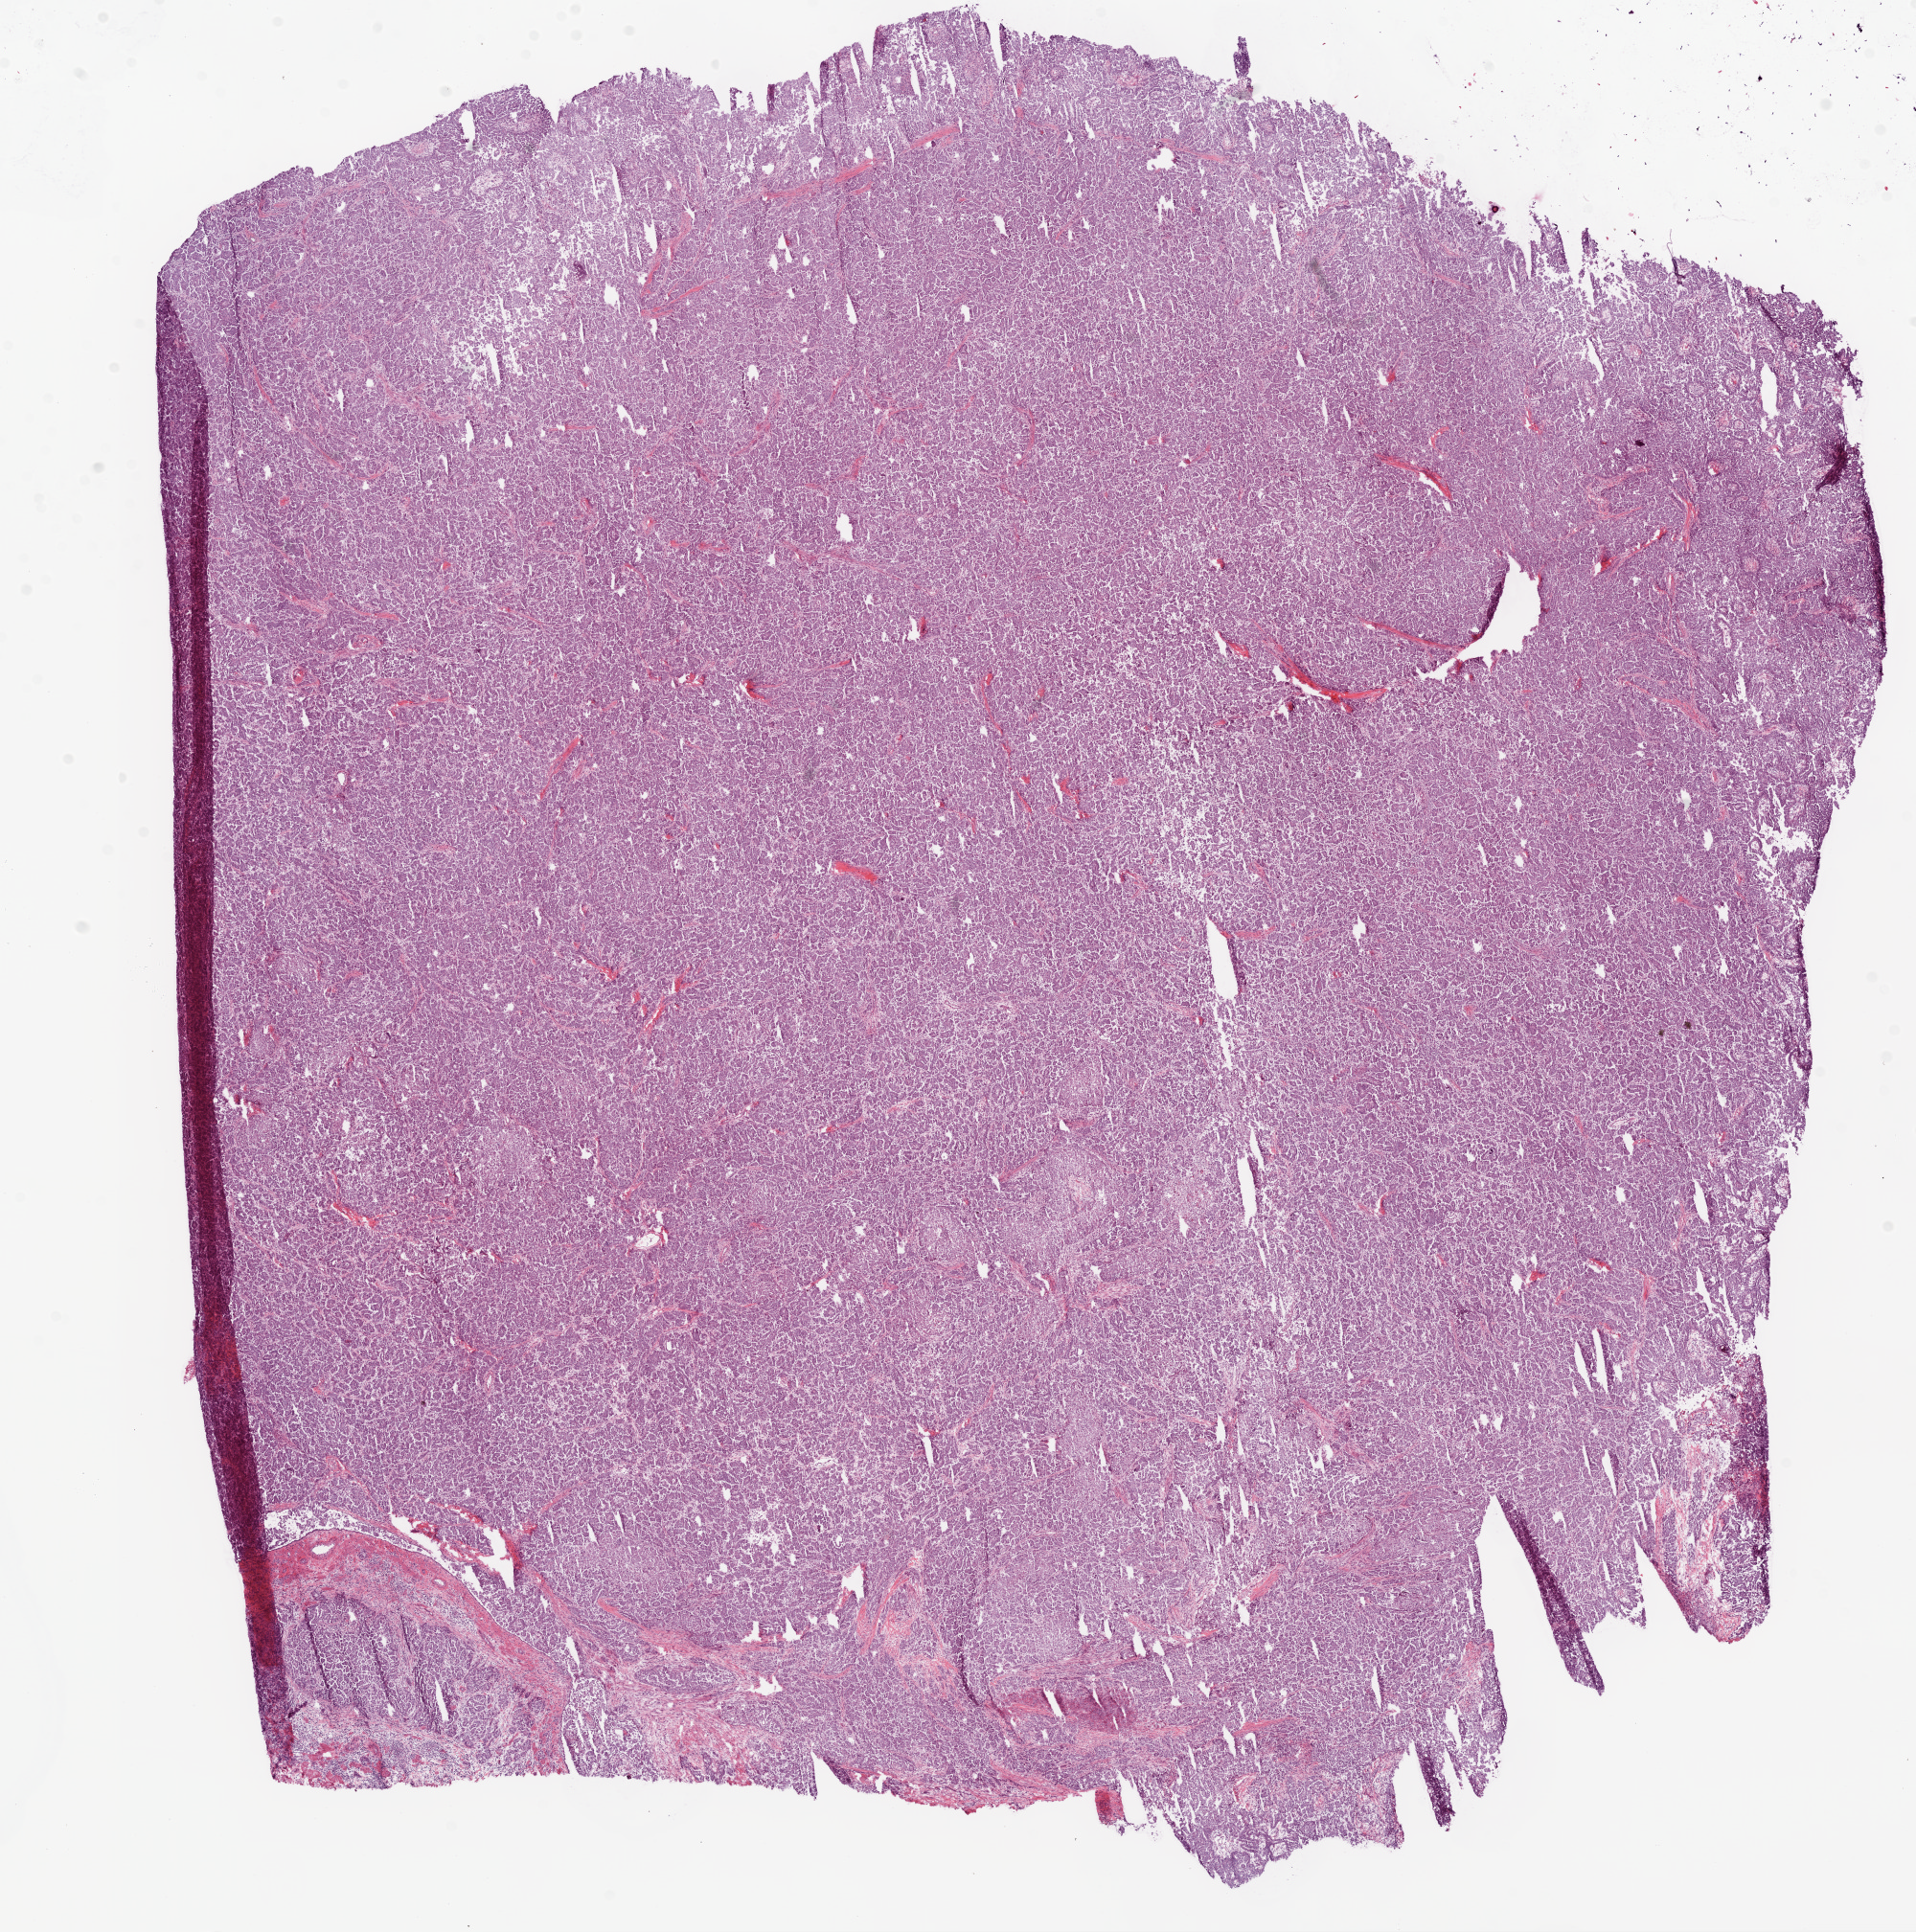
Digitized H&E tissue section (whole slide), whole scanned area (about 16.0 x 16.2 mm) shown as a low-resolution overview. Frozen section. Primary tumour sample from the ovary. Female, age 71 years at initial diagnosis. Histologic grade: G3 (poorly differentiated). Composition of this section per pathologist review: tumour cells 94%, tumour nuclei 95%, normal cells 1%, stromal cells 4%, necrosis 1%.
• FIGO stage: IV
• diagnosis: Serous cystadenocarcinoma, NOS